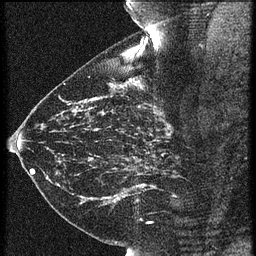
Breast MRI (dynamic contrast-enhanced), one sagittal slice. Slice 36 of 60 in the series (ordered by position). 3 images stored at this slice position (order not interpretable as contrast timing). 1.5 T. TE 4.2 ms, TR 21.3 ms. 256 × 256 image matrix. Patient: female, 43 years. From the clinical record (not read from this slice): setting: breast cancer imaged before/during neoadjuvant chemotherapy; receptor status: HER2-positive.
Annotated regions visible in this slice (semi-automatically segmented with operator editing):
- analysis volume of interest (the breast-tissue region the enhancement analysis was run in; not a lesion): bounding box <119,114,189,173> (left, top, right, bottom; pixels)
- tumour enhancement mask (voxels above the 90 % enhancement threshold inside the analysis volume of interest): <158,114,172,133>